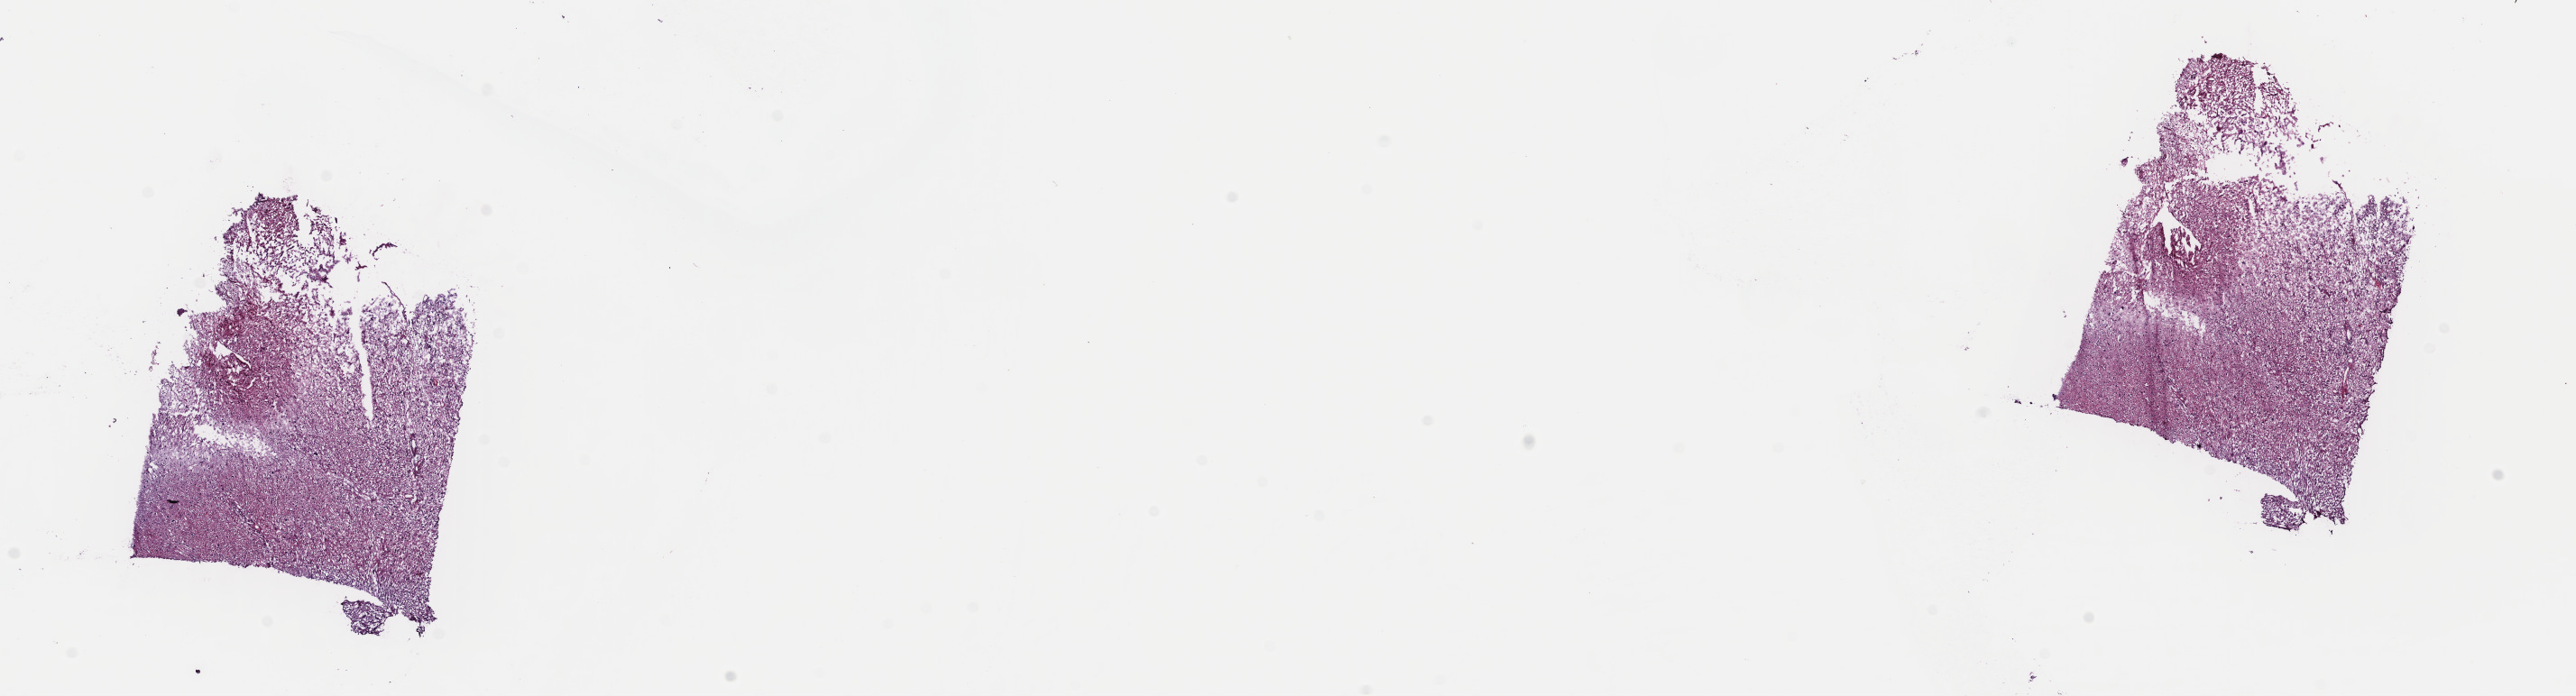
H&E-stained whole-slide image — low-resolution overview of the scanned area, about 22.5 x 6.1 mm (slide scanned at 40x). Frozen section from the top of the tissue portion. Primary tumour sample from the brain. Female, age 25 years at initial diagnosis. Histologic grade: G2 (moderately differentiated). Slide review estimates, as recorded: tumour cells 45%, tumour nuclei 80%, normal cells 10%, stromal cells 45%, necrosis 0%. Inflammatory infiltration, as recorded: lymphocyte infiltration 5%, monocyte infiltration 5%, neutrophil infiltration 0%.
Laterality: right. Diagnosis: Astrocytoma, NOS (cerebrum).